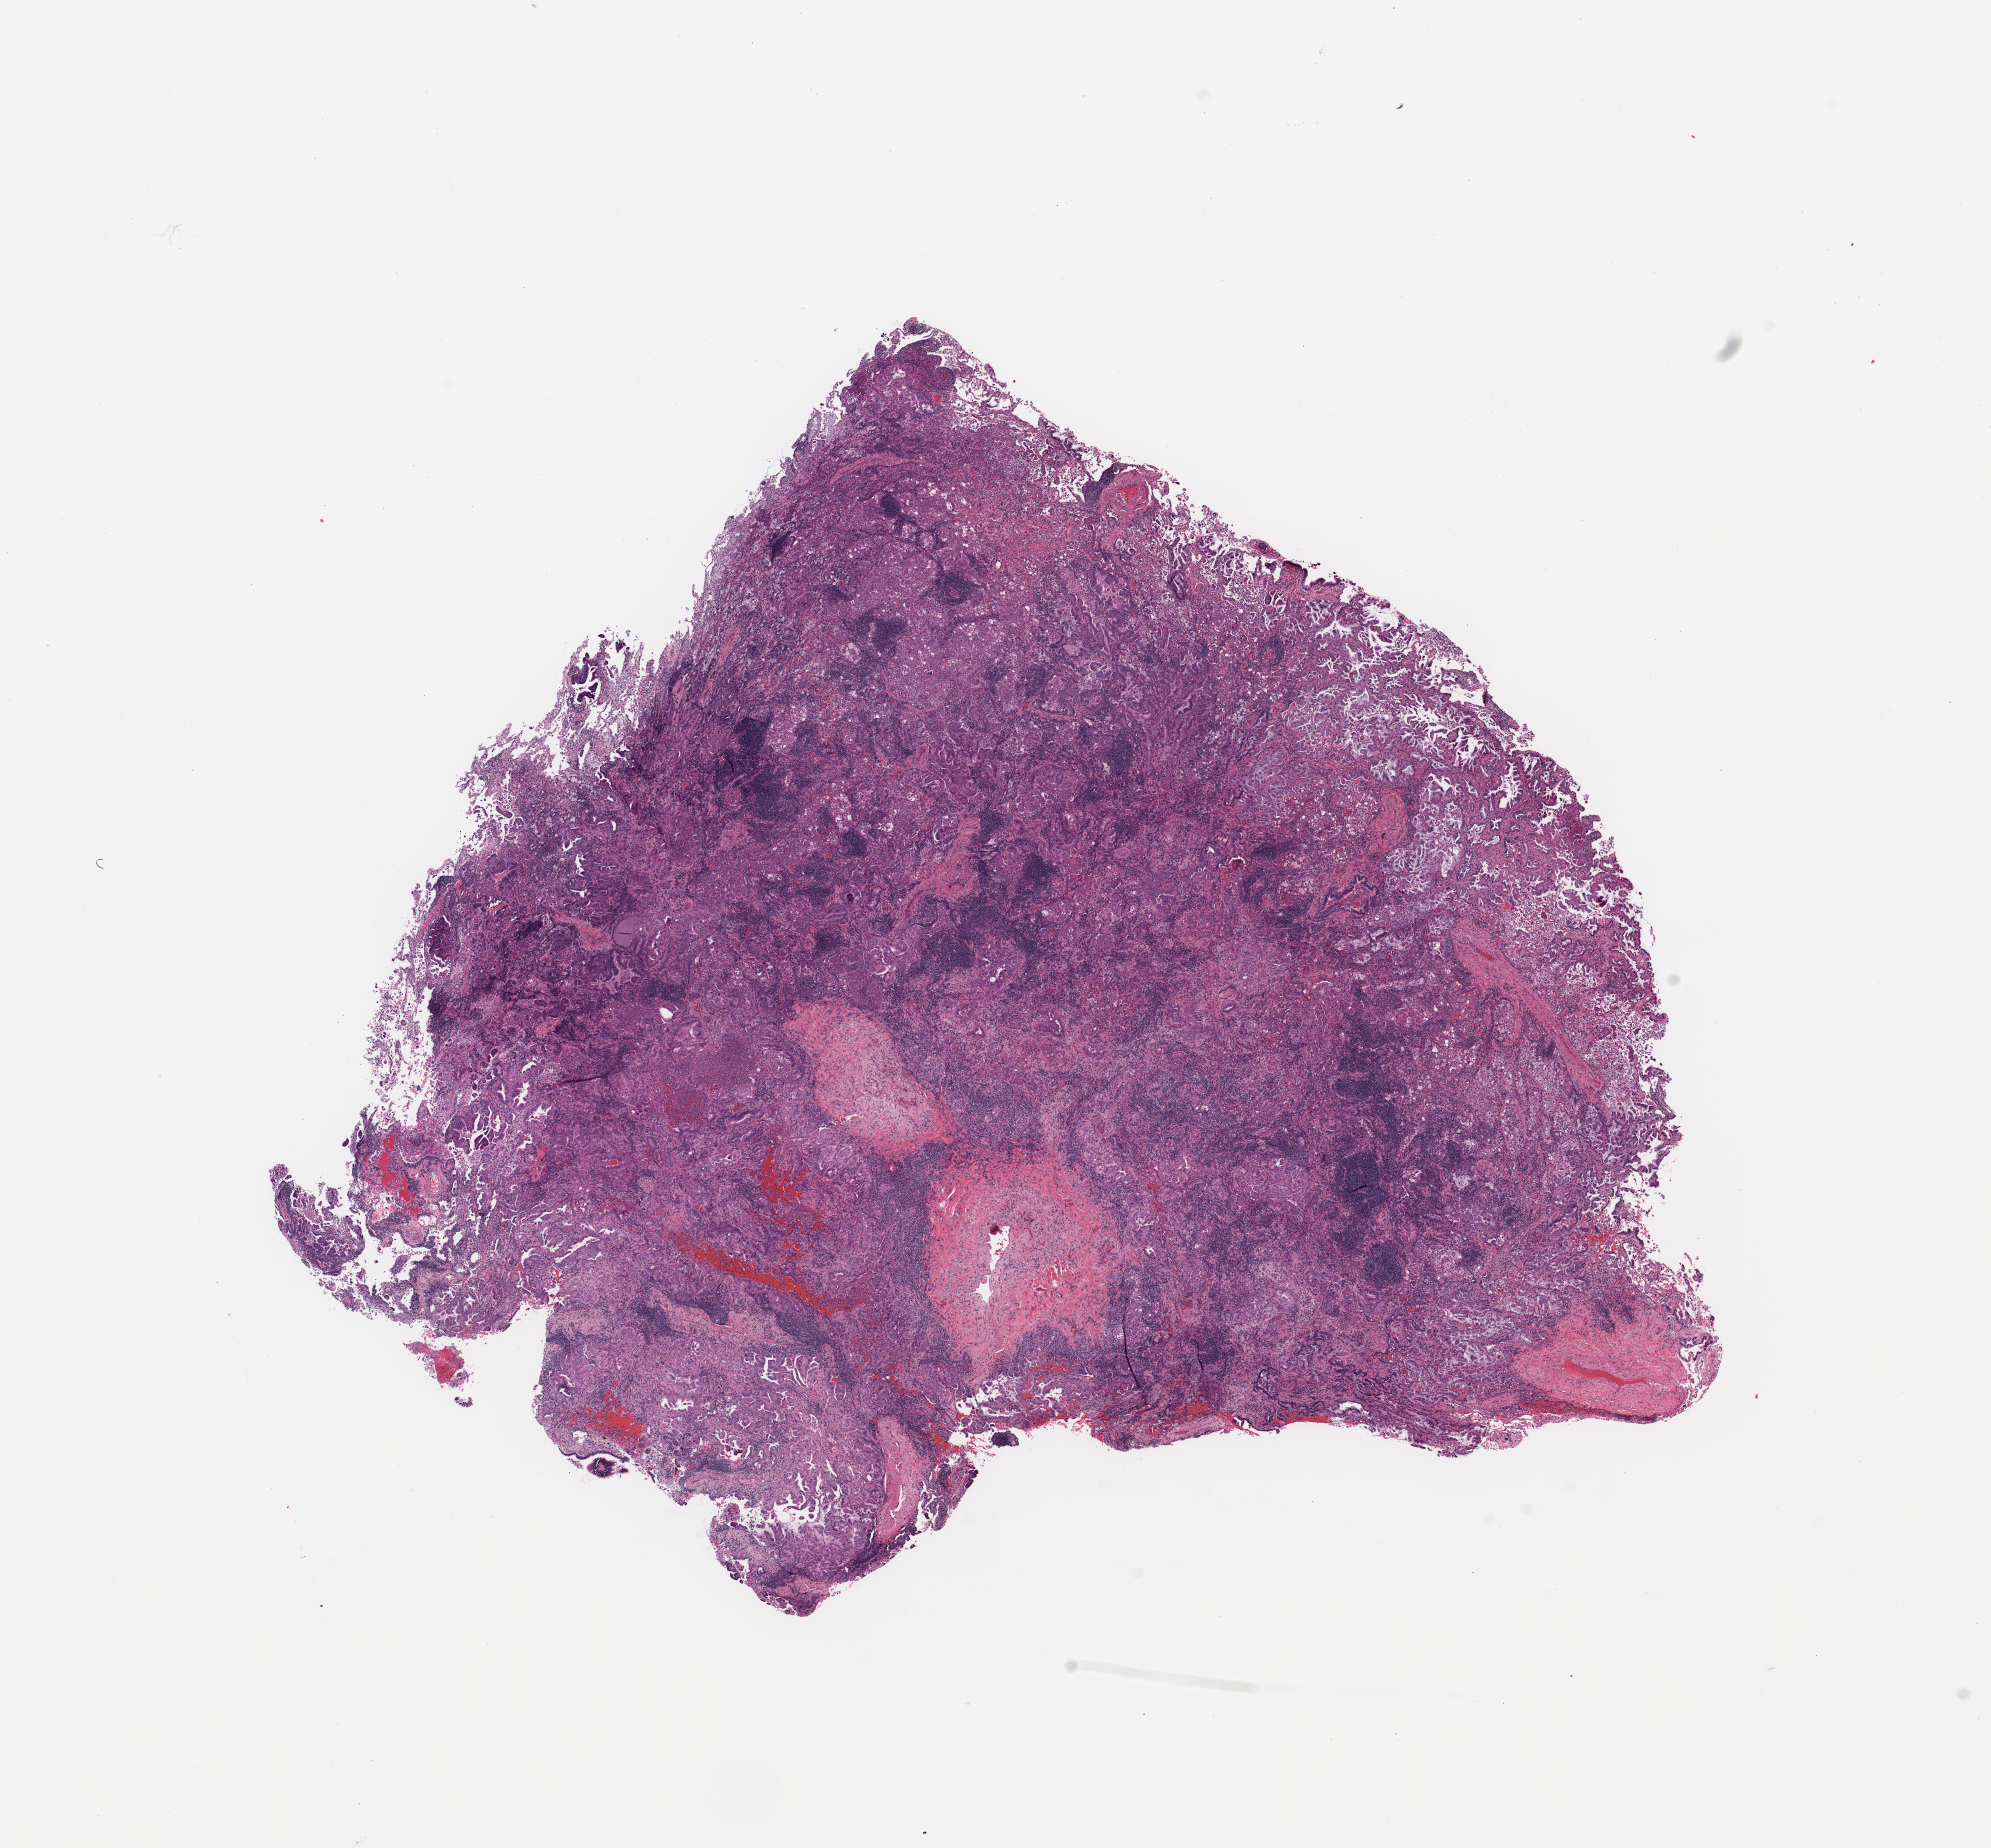
Whole-slide histology image, H&E-stained — whole scanned area (about 15.8 x 14.6 mm) shown as a low-resolution overview; lung, tumour tissue. Patient: male, age 76 years. Histologic grade: G2 (moderately differentiated).
Diagnosis: Adenocarcinoma, NOS. Primary tumour site (as recorded): right lower lobe. AJCC pathologic stage: IB.